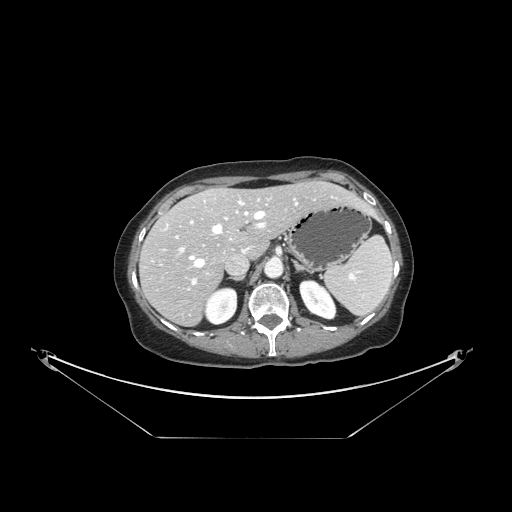
Contrast-enhanced abdominal CT, one axial slice; slice 99 of 148 in the series (ordered by position); reconstruction kernel STANDARD; 120 kVp; intravenous contrast given; soft-tissue window (W 400 / L 40 HU); 2.5 mm slice thickness; 512 × 512 image matrix, field of view 500 × 500 mm. Female patient, age 73 years. From the clinical record (not read from this slice): diagnosis: colorectal cancer liver metastases, imaged before liver resection; multiple liver metastases: no; largest metastasis: 1 cm; disease in both lobes: no.
Outlined on this slice (outlined manually by an expert reader):
- hepatic veins: box from (x=165, y=196) to (x=333, y=267) px
- liver: (x=142, y=182)–(x=367, y=325)
- planned liver remnant (the part of the liver to remain after resection): (x=168, y=182)–(x=366, y=257)
- portal vein (with intrahepatic branches): (x=176, y=204)–(x=267, y=285)